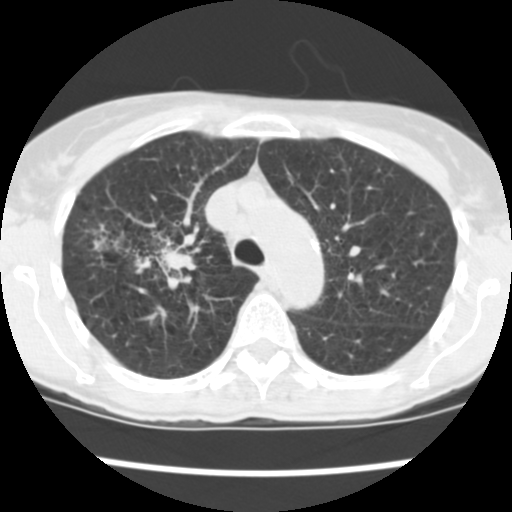
Axial slice from a low-dose chest CT screening exam. Baseline annual screen. Lung window (W 1500 / L -600 HU). Standard (soft-tissue) reconstruction kernel (STANDARD). Slice 179 of 252 in the series. 512 × 512 image matrix. Female, age 60 years at enrolment. Current smoker at enrolment.
- Expert-annotated lung lesion, box from (x=85, y=216) to (x=202, y=286) px.
- The screening reader recorded 3 non-calcified nodules or masses ≥4 mm on this exam (right upper lobe, right upper lobe, right lower lobe); which of them this box marks is not recorded.
- Lung cancer was diagnosed 19 days after this screen: non-small cell carcinoma, right upper lobe, stage IV (AJCC 6th edition), 26 mm at pathology.